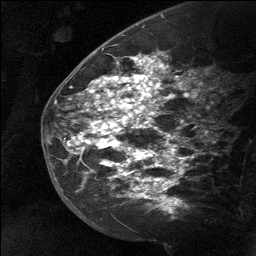
Breast MRI (dynamic contrast-enhanced), one sagittal slice; position 40 of 64 along the scan axis; dynamic contrast-enhanced study with each time point stored as its own series, time point 2 of 3 at this slice position (early post-contrast, ordered by acquisition time); 1.5 T; TE 4.8 ms, TR 27 ms; 2 mm slice thickness; 256 × 256 image matrix, field of view 180 × 180 mm. Female patient, age 39 years. Case-level facts recorded for this patient, not image findings: setting: breast cancer imaged before/during neoadjuvant chemotherapy; receptor status: HER2-positive.
Annotated regions visible in this slice (semi-automatically segmented with operator editing):
- analysis volume of interest (the breast-tissue region the enhancement analysis was run in; not a lesion): bounding box [x1, y1, x2, y2] px = [58, 40, 178, 217]
- tumour enhancement mask (voxels above the 90 % enhancement threshold inside the analysis volume of interest): [67, 54, 174, 200]